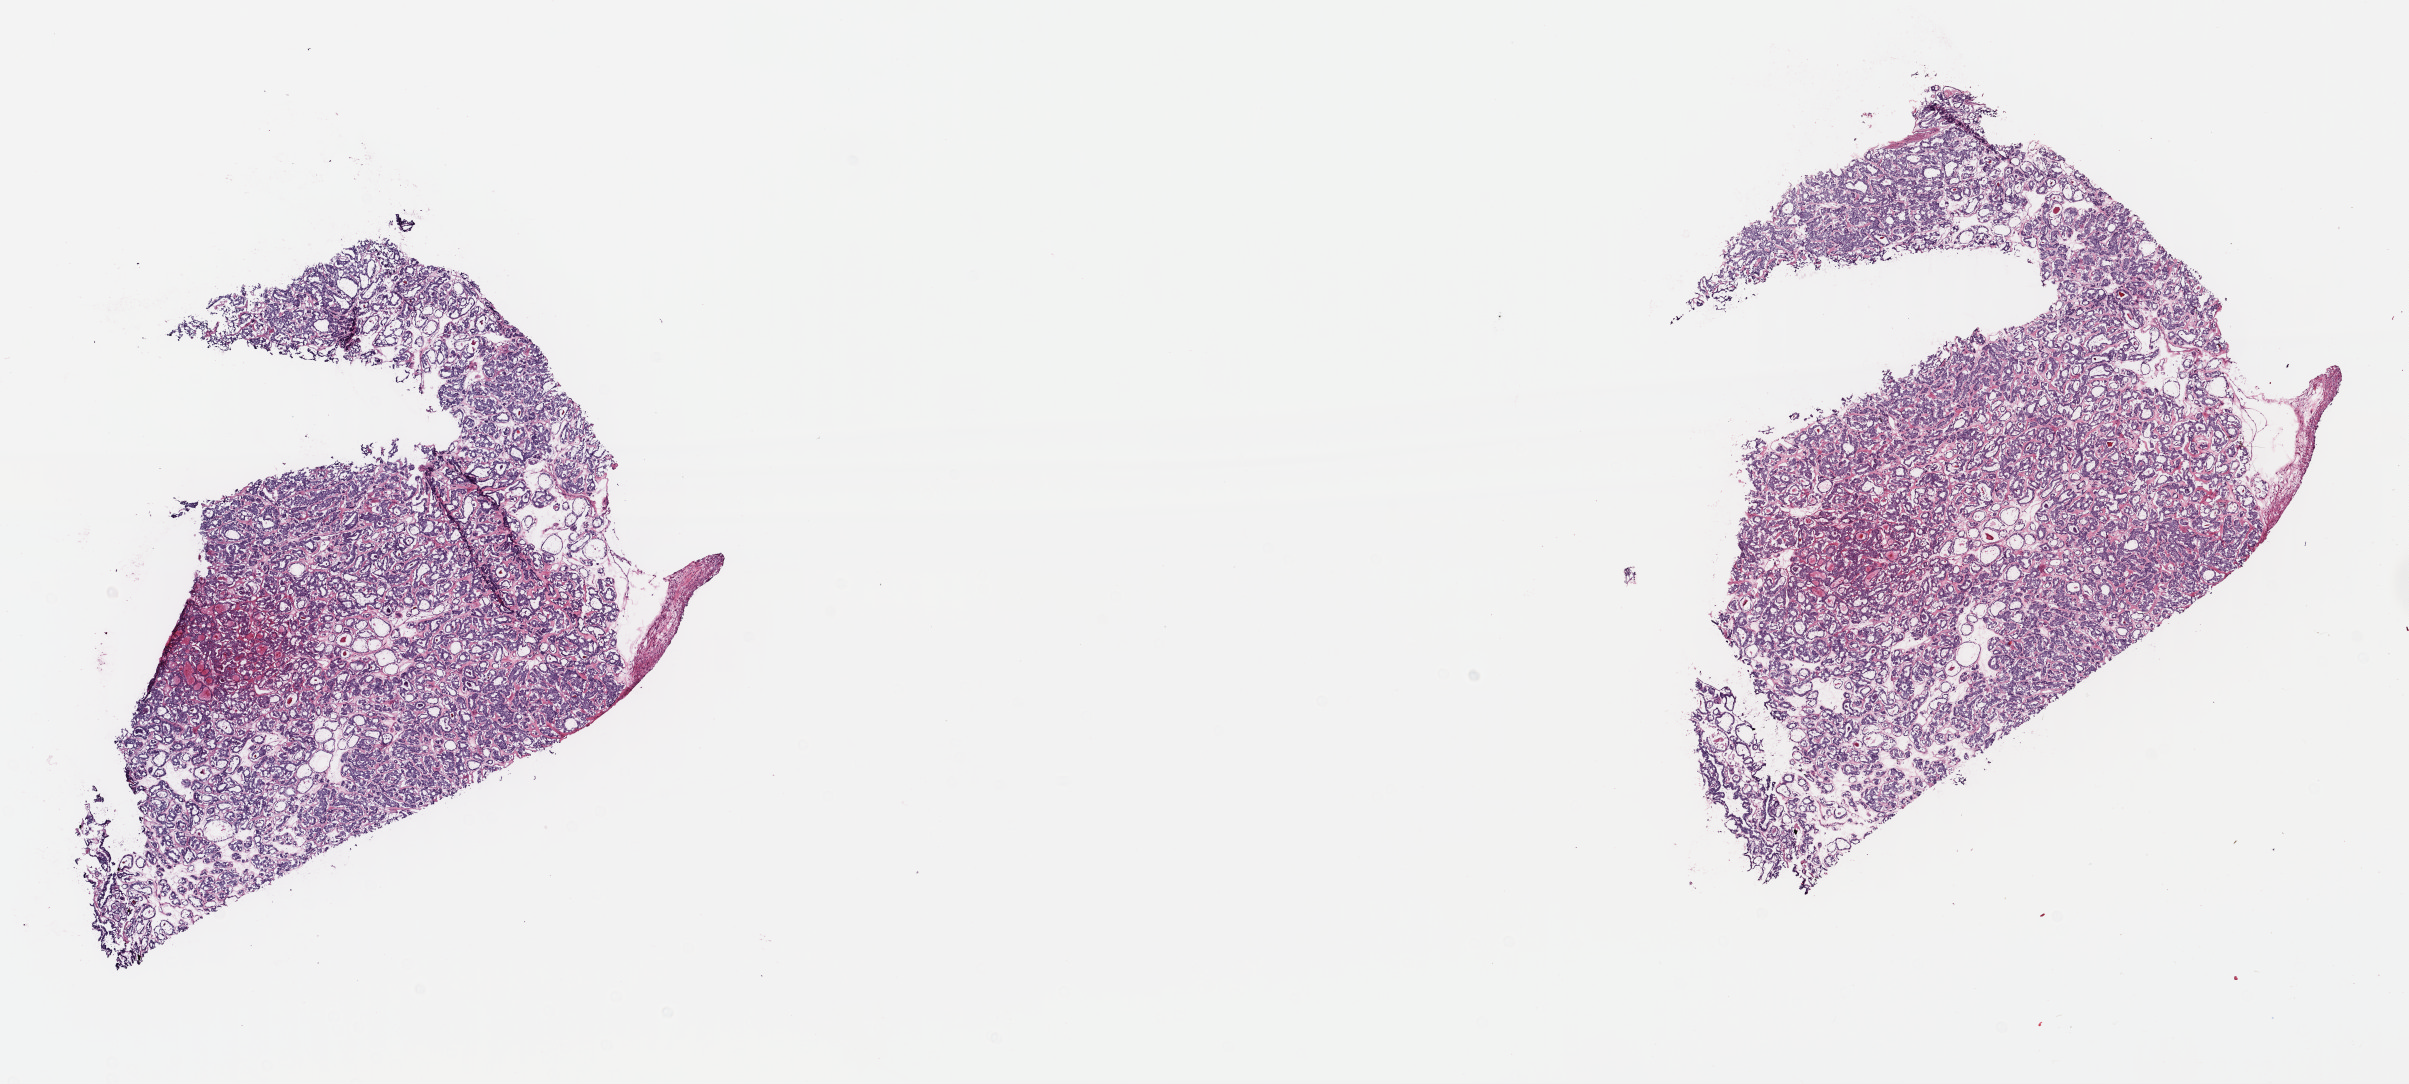
H&E whole-slide image, whole scanned area (about 18.9 x 8.5 mm, from a 40x scan) shown as a low-resolution overview. Frozen section. Sample: primary tumour, thyroid. Female patient; age at initial diagnosis 53 years. Slide review estimates, as recorded: tumour cells 100%, tumour nuclei 95%, normal cells 0%, stromal cells 0%, necrosis 0%. Infiltration values recorded for this section: lymphocyte infiltration 0%, monocyte infiltration 0%, neutrophil infiltration 0%.
TNM: T3 N0 MX. AJCC pathologic stage: III (6th edition). Histologic diagnosis: Papillary carcinoma, follicular variant (thyroid gland). Lymph nodes positive (case pathology): 0 of 2 examined.